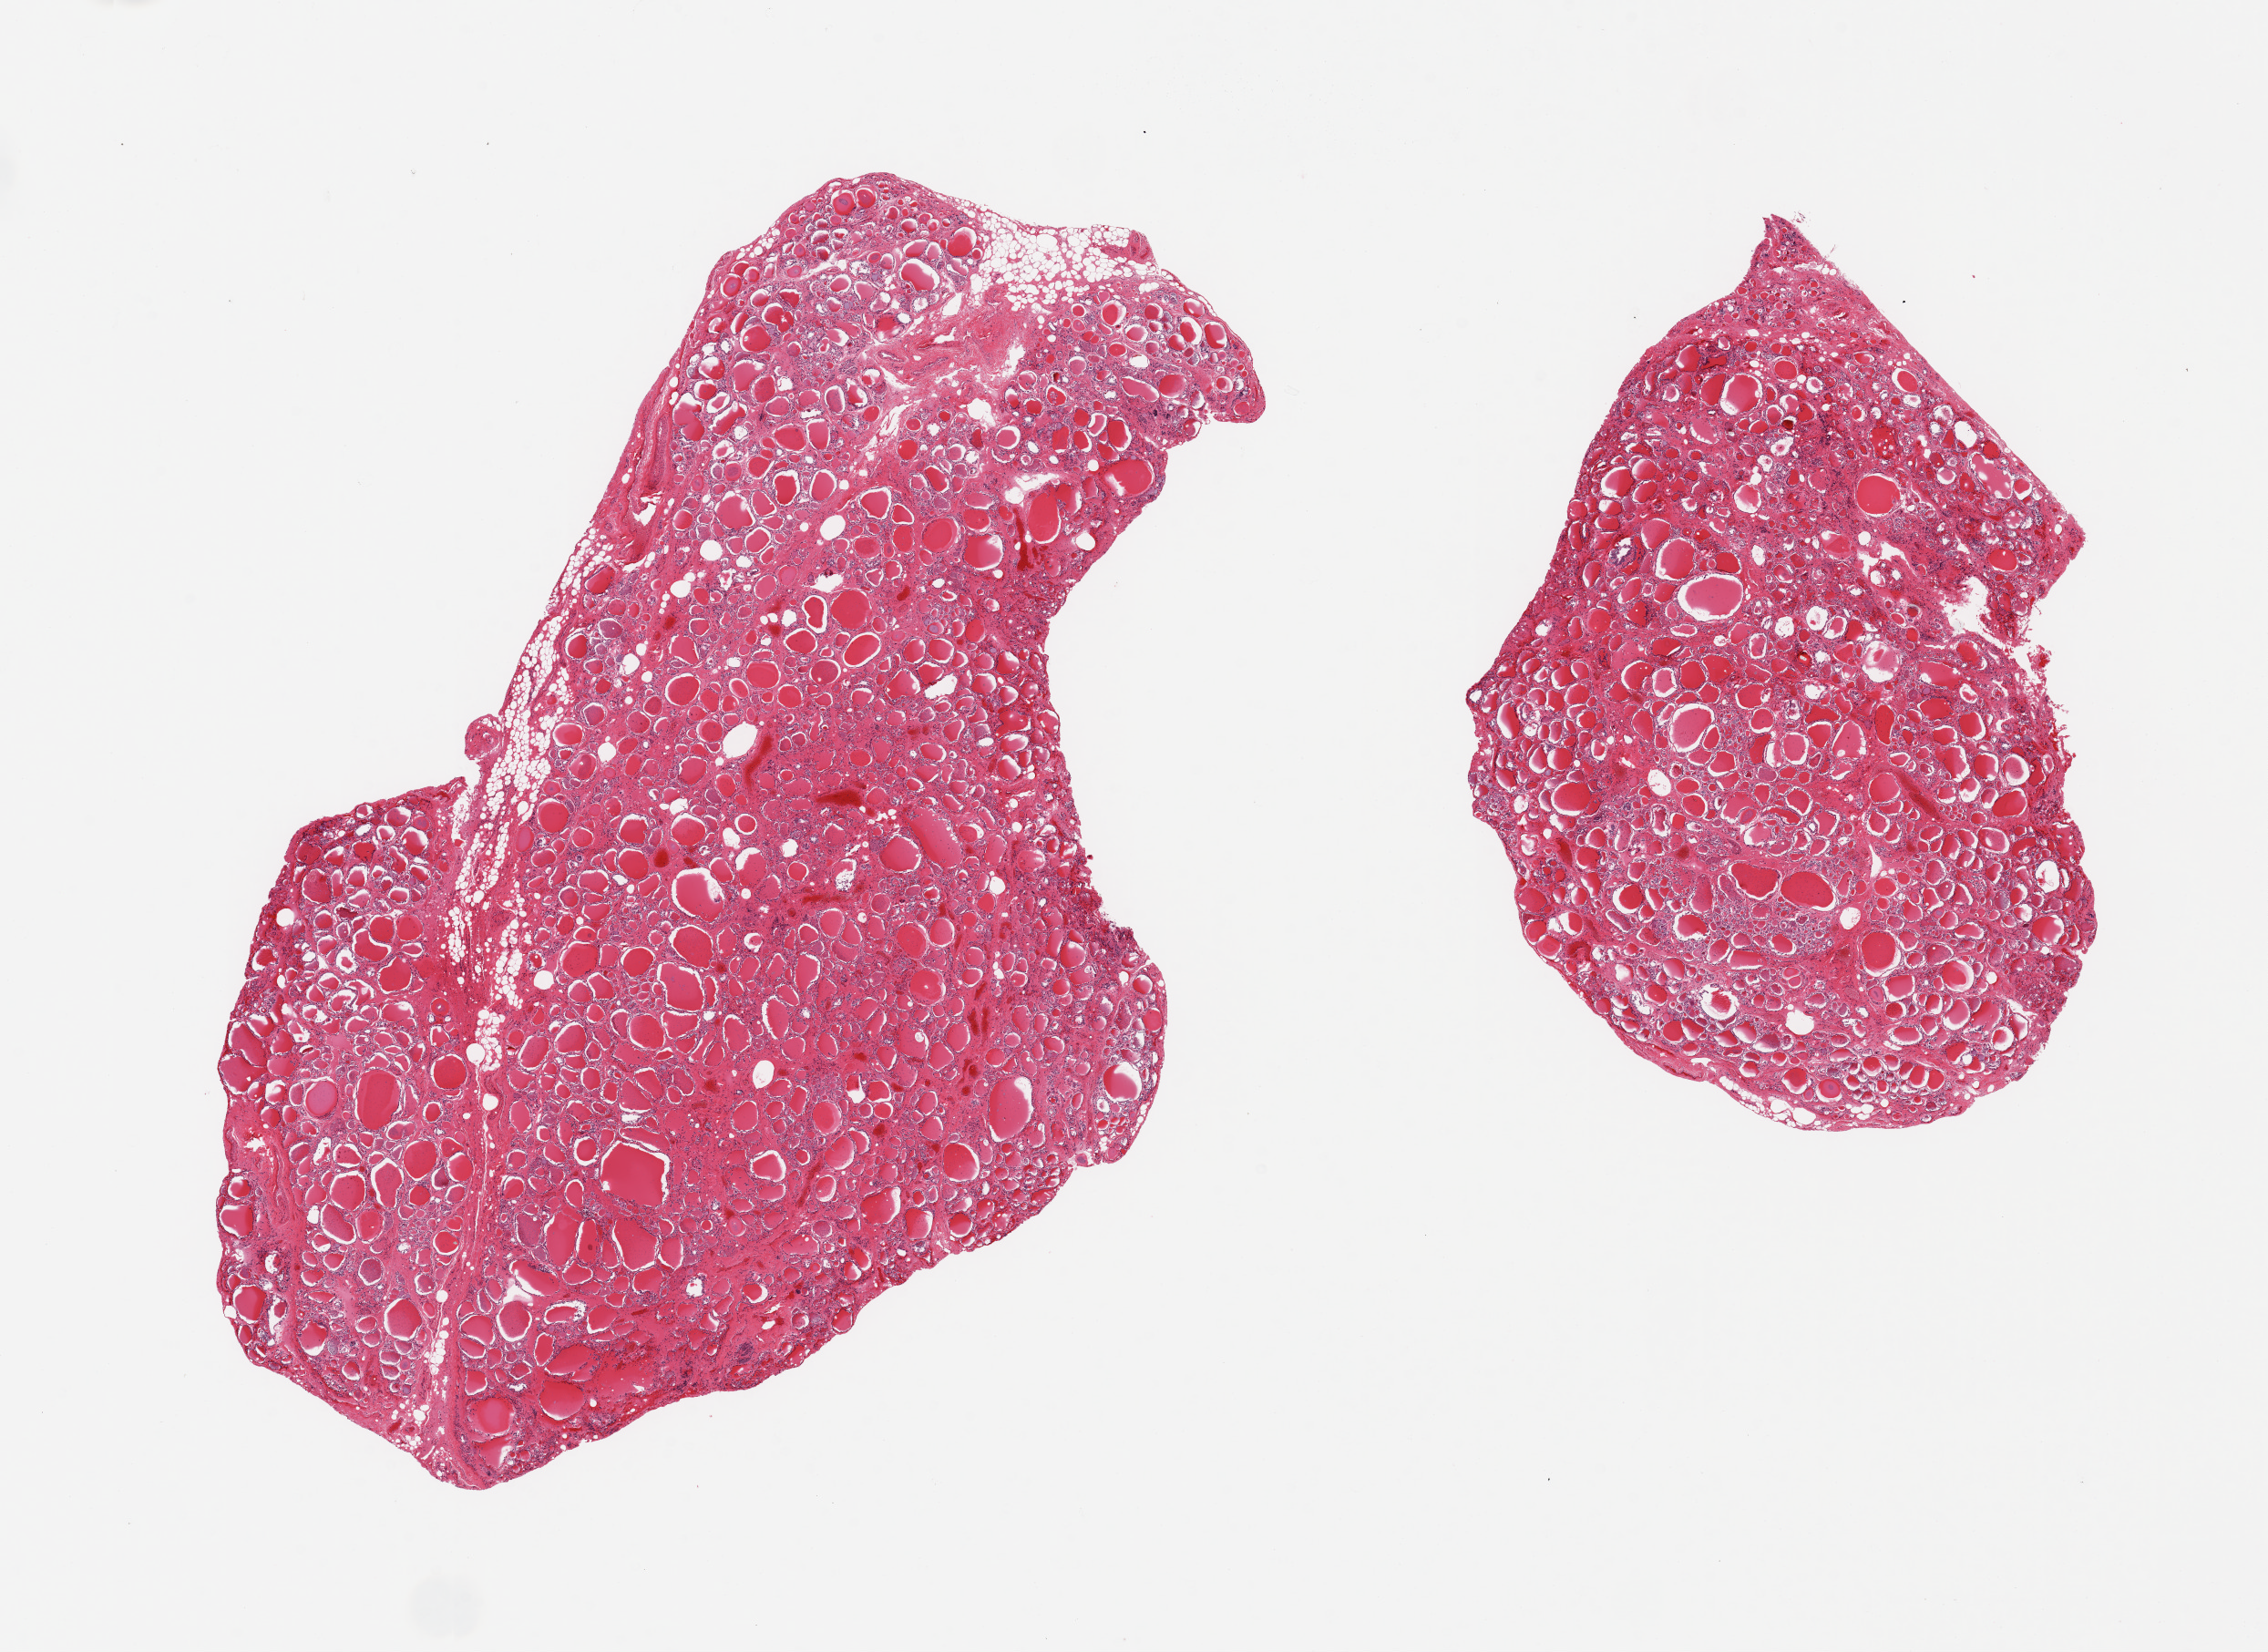
Digitized hematoxylin and eosin (H&E)-stained section — low-resolution overview of the scanned area, about 19.7 x 14.3 mm; PAXgene-fixed, paraffin-embedded tissue; target tissue: thyroid; donor tissue sample.
• pathologist's review note for this sample: 2 pieces; mild interstitial fibrosis, small component of fat